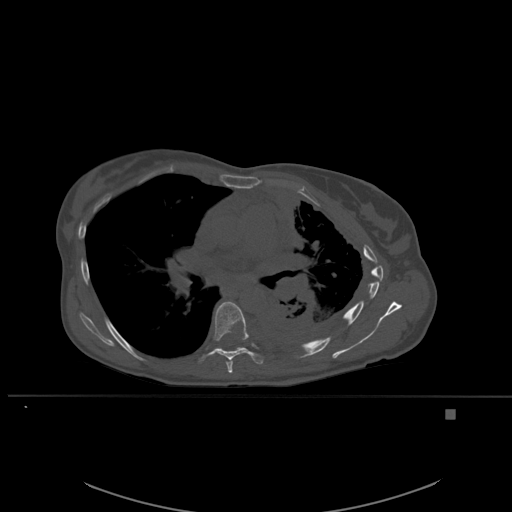
CT including the spine, one axial slice; slice 367 of 537 in the series (ordered by position); bone window (W 1800 / L 400 HU); 1.5 mm slice thickness; 512 × 512 image matrix, field of view 440 × 440 mm. Patient: female, 45 years. From the clinical record (not read from this slice): primary cancer: lung.
Structures marked on this image (semi-automatically segmented with operator editing):
- T6 vertebra: bounding box [x1, y1, x2, y2] px = [225, 360, 233, 373]
- T7 vertebra: [200, 301, 264, 364]